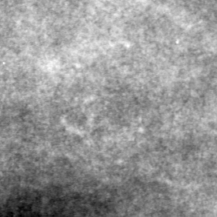
Crop from a digitized film mammogram around one marked abnormality; left breast; MLO view.
- Marked abnormality: calcifications, morphology pleomorphic, distribution clustered; BI-RADS assessment category 4; subtlety rating 3 on a 1 (subtle) to 5 (obvious) scale; pathology (as recorded): malignant.